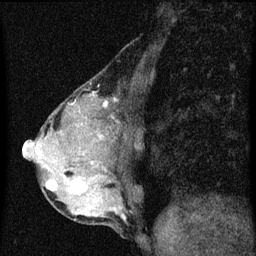
Breast MRI (dynamic contrast-enhanced), one sagittal slice. Position 21 of 60 along the scan axis. Dynamic contrast-enhanced series, image 2 of 3 at this slice position (ordered by acquisition). 1.5 T. TE 4.2 ms, TR 8 ms. 2 mm slice thickness. 256 × 256 image matrix. Female patient, age 49 years.
Structures marked on this image (semi-automatically segmented with operator editing):
- analysis volume of interest (the breast-tissue region the enhancement analysis was run in; not a lesion): box from (x=44, y=174) to (x=89, y=201) px
- tumour enhancement mask (voxels above the 70 % enhancement threshold inside the analysis volume of interest): (x=46, y=180)–(x=86, y=193)